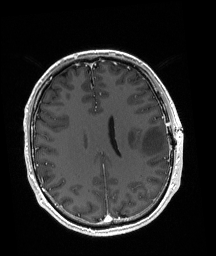
Brain MRI from a brain-tumour surgery series, one axial slice. Position 74 of 192 along the scan axis. T1-weighted post-contrast. 216 × 256 image matrix, field of view 211 × 250 mm. From the clinical record (not read from this slice): histopathology: Astrocytoma; WHO grade: 3; IDH mutation: yes.
Annotated regions visible in this slice (expert manual segmentation):
- tumour: bounding box (x1, y1, x2, y2) in pixels: (127, 126, 166, 155)